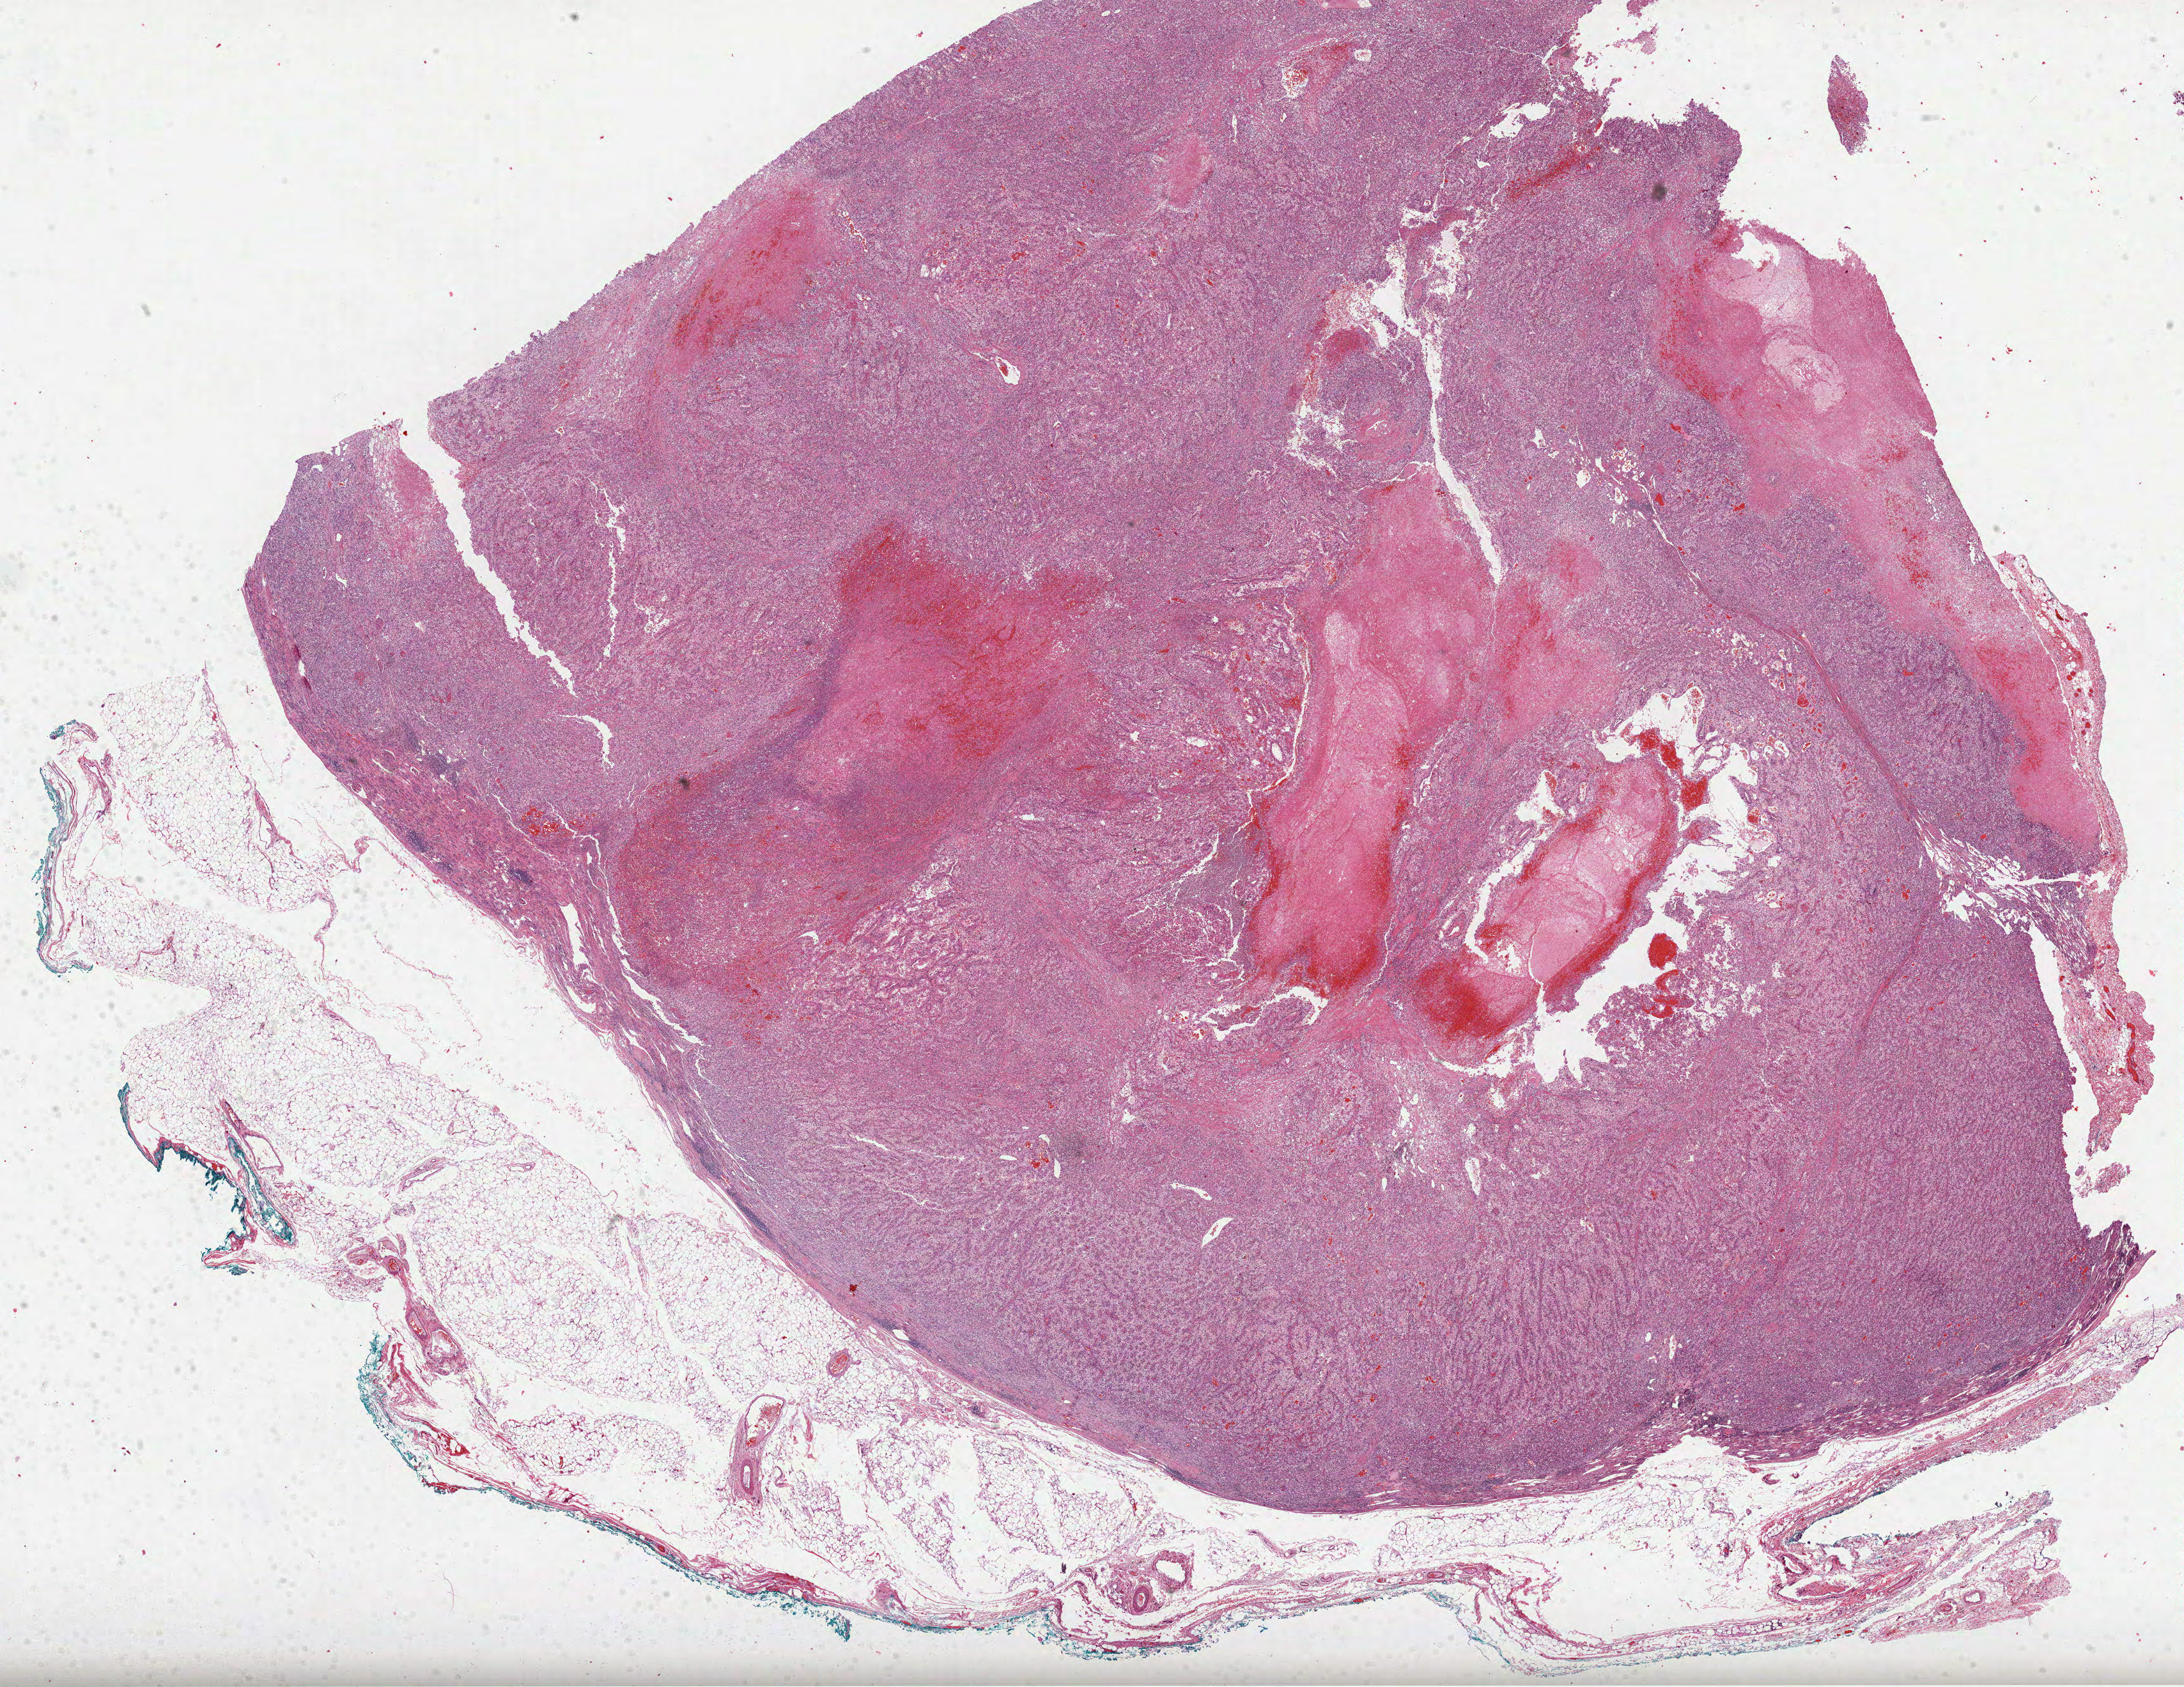
Whole-slide histology image, H&E-stained — a low-resolution overview of the entire scanned area, about 27.6 x 21.3 mm; formalin-fixed paraffin-embedded (FFPE) diagnostic section; sample: primary tumour, kidney. Male patient; age at initial diagnosis 76 years. Histologic grade: G3 (poorly differentiated).
• diagnosis: Clear cell adenocarcinoma, NOS
• TNM: T3a NX M1
• AJCC pathologic stage: IV